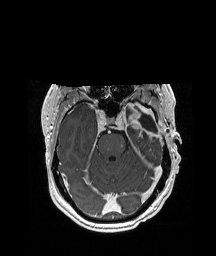
Brain MRI from a brain-tumour surgery series, one axial slice. Position 135 of 208 along the scan axis. T1-weighted post-contrast. 1 mm slice thickness. 216 × 256 image matrix. From the clinical record (not read from this slice): histopathology: Glioblastoma; WHO grade: 4; IDH mutation: no.
Annotated regions visible in this slice (outlined manually by an expert reader):
- previous resection cavity: bounding box <135,106,158,134> (left, top, right, bottom; pixels)
- tumour: <123,99,158,134>